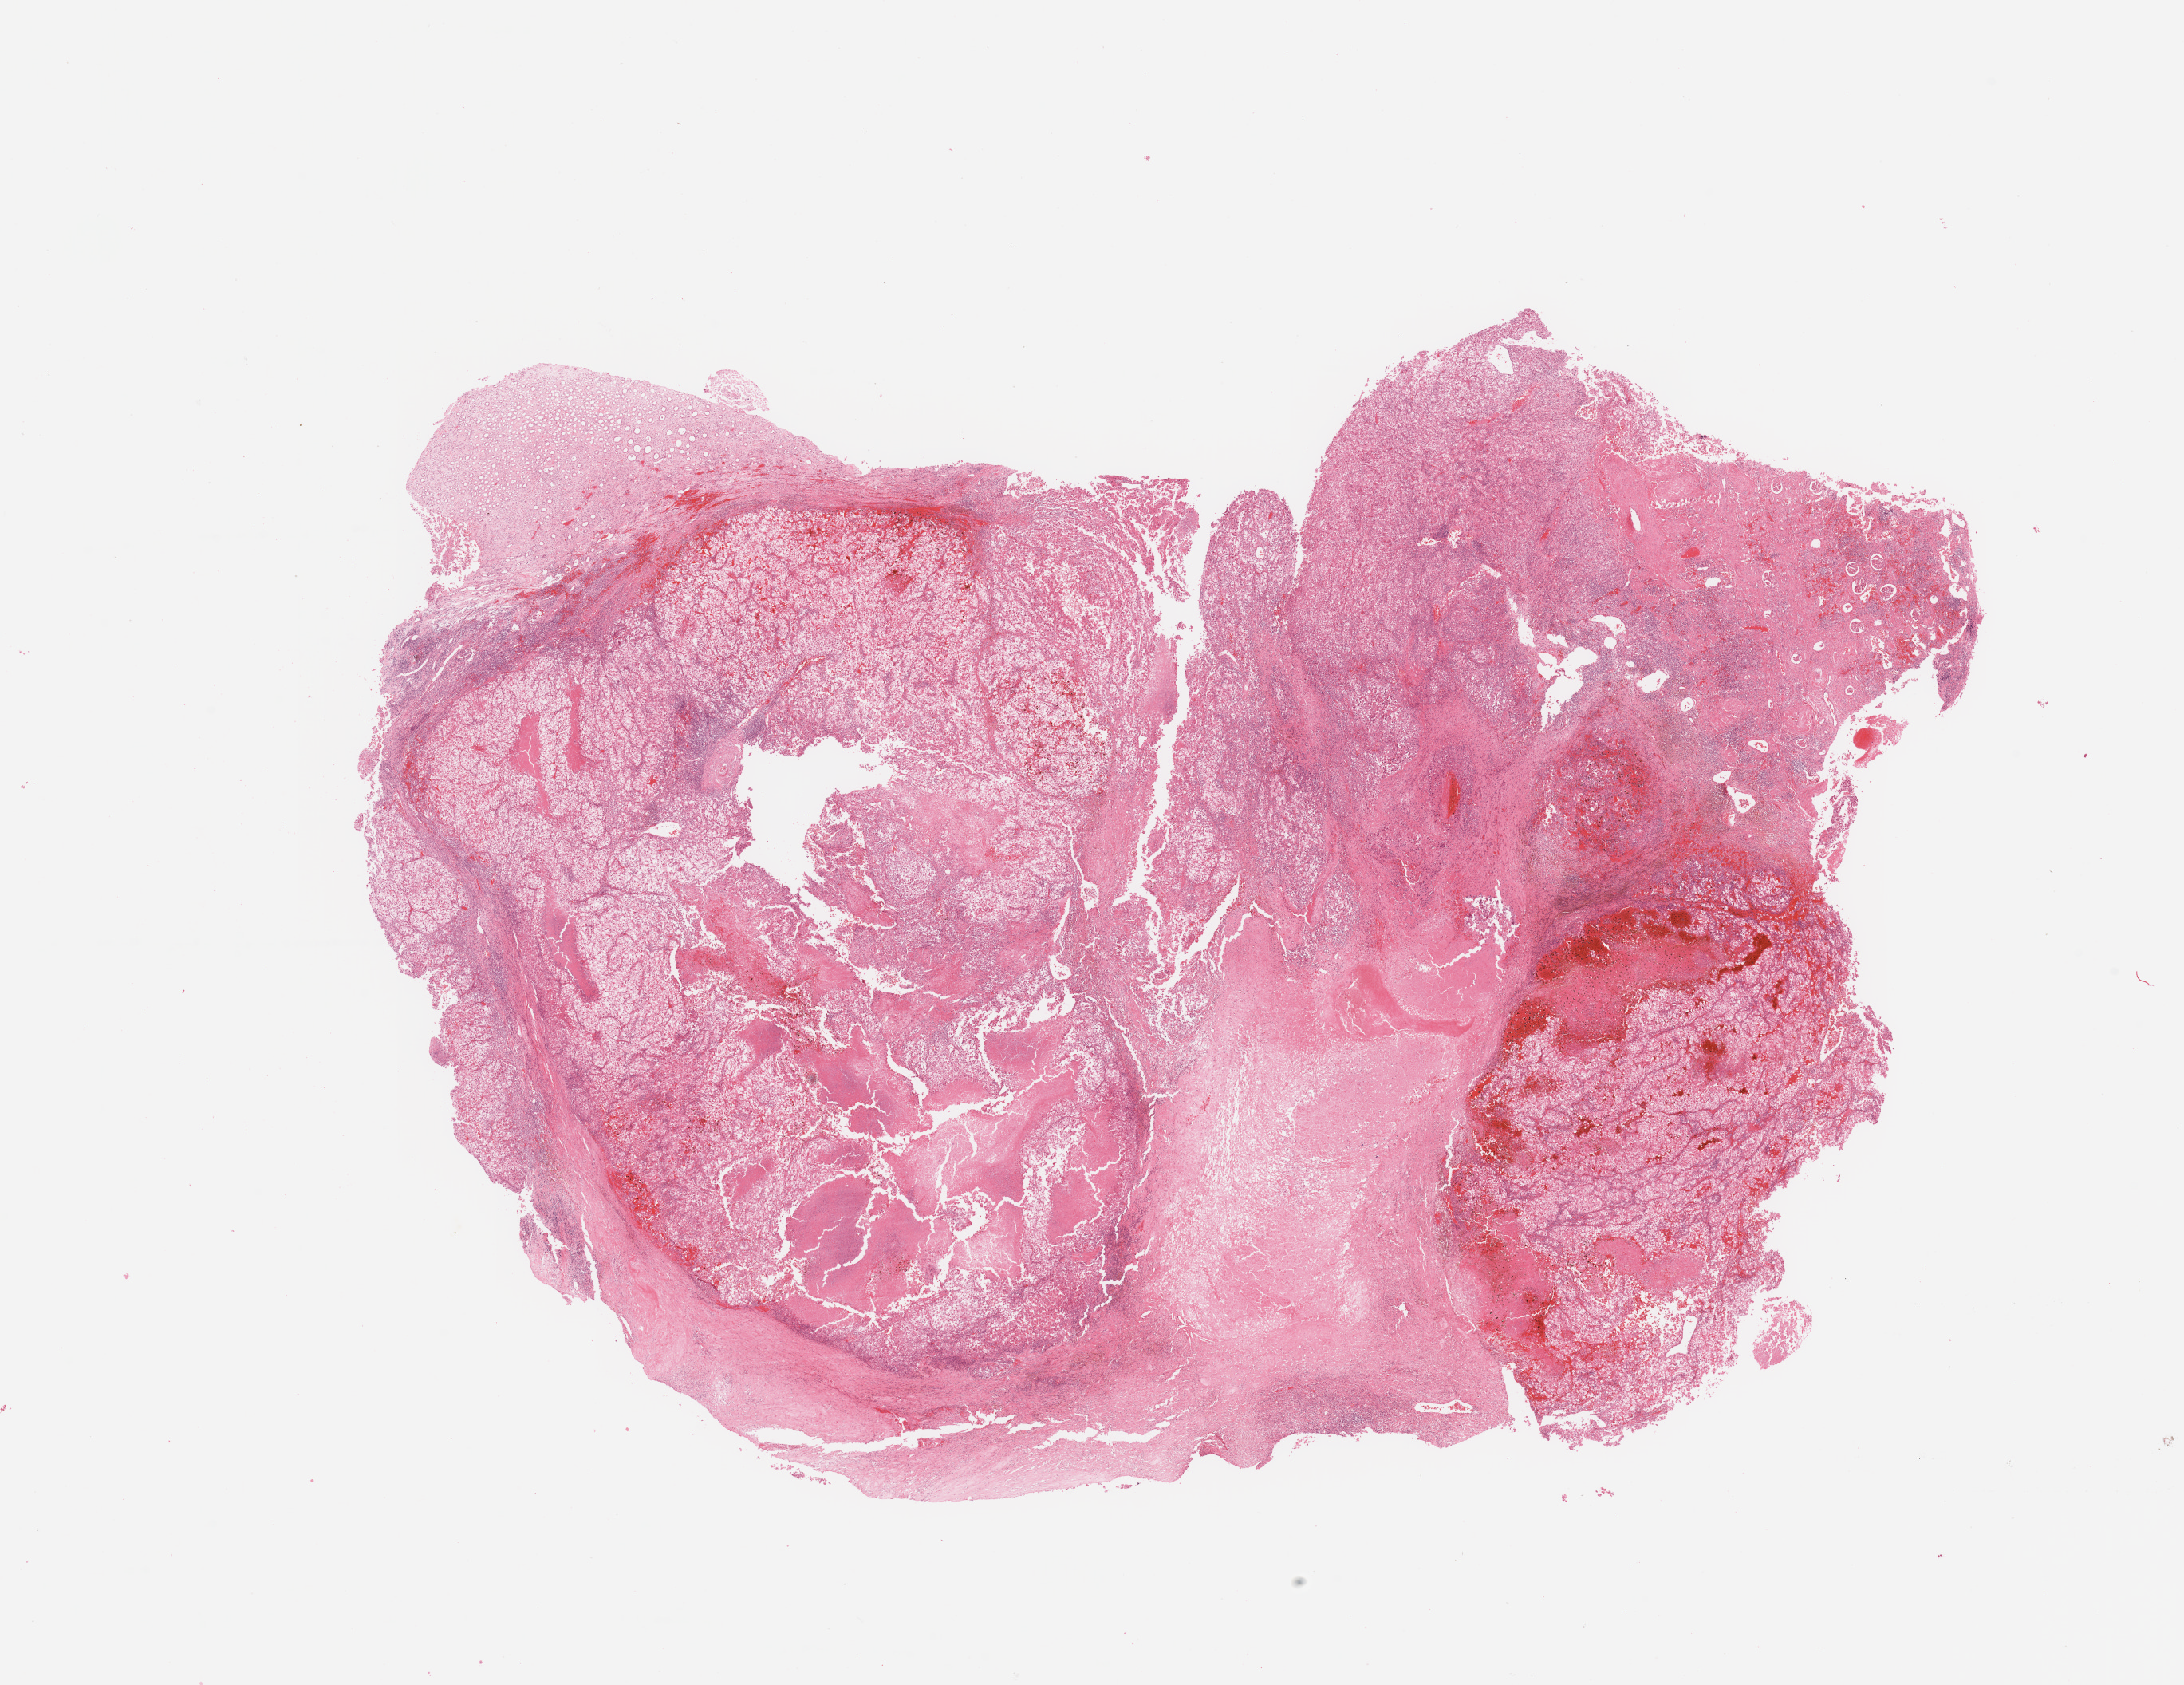
Digitized Hematoxylin and eosin (H&E) stained tissue section (whole slide) — whole scanned area (about 21.7 x 16.7 mm) shown as a low-resolution overview; tumour tissue sample, kidney. Patient: female, age 52 years. Histologic grade: G2 (moderately differentiated).
Diagnosis: Renal cell carcinoma, NOS.